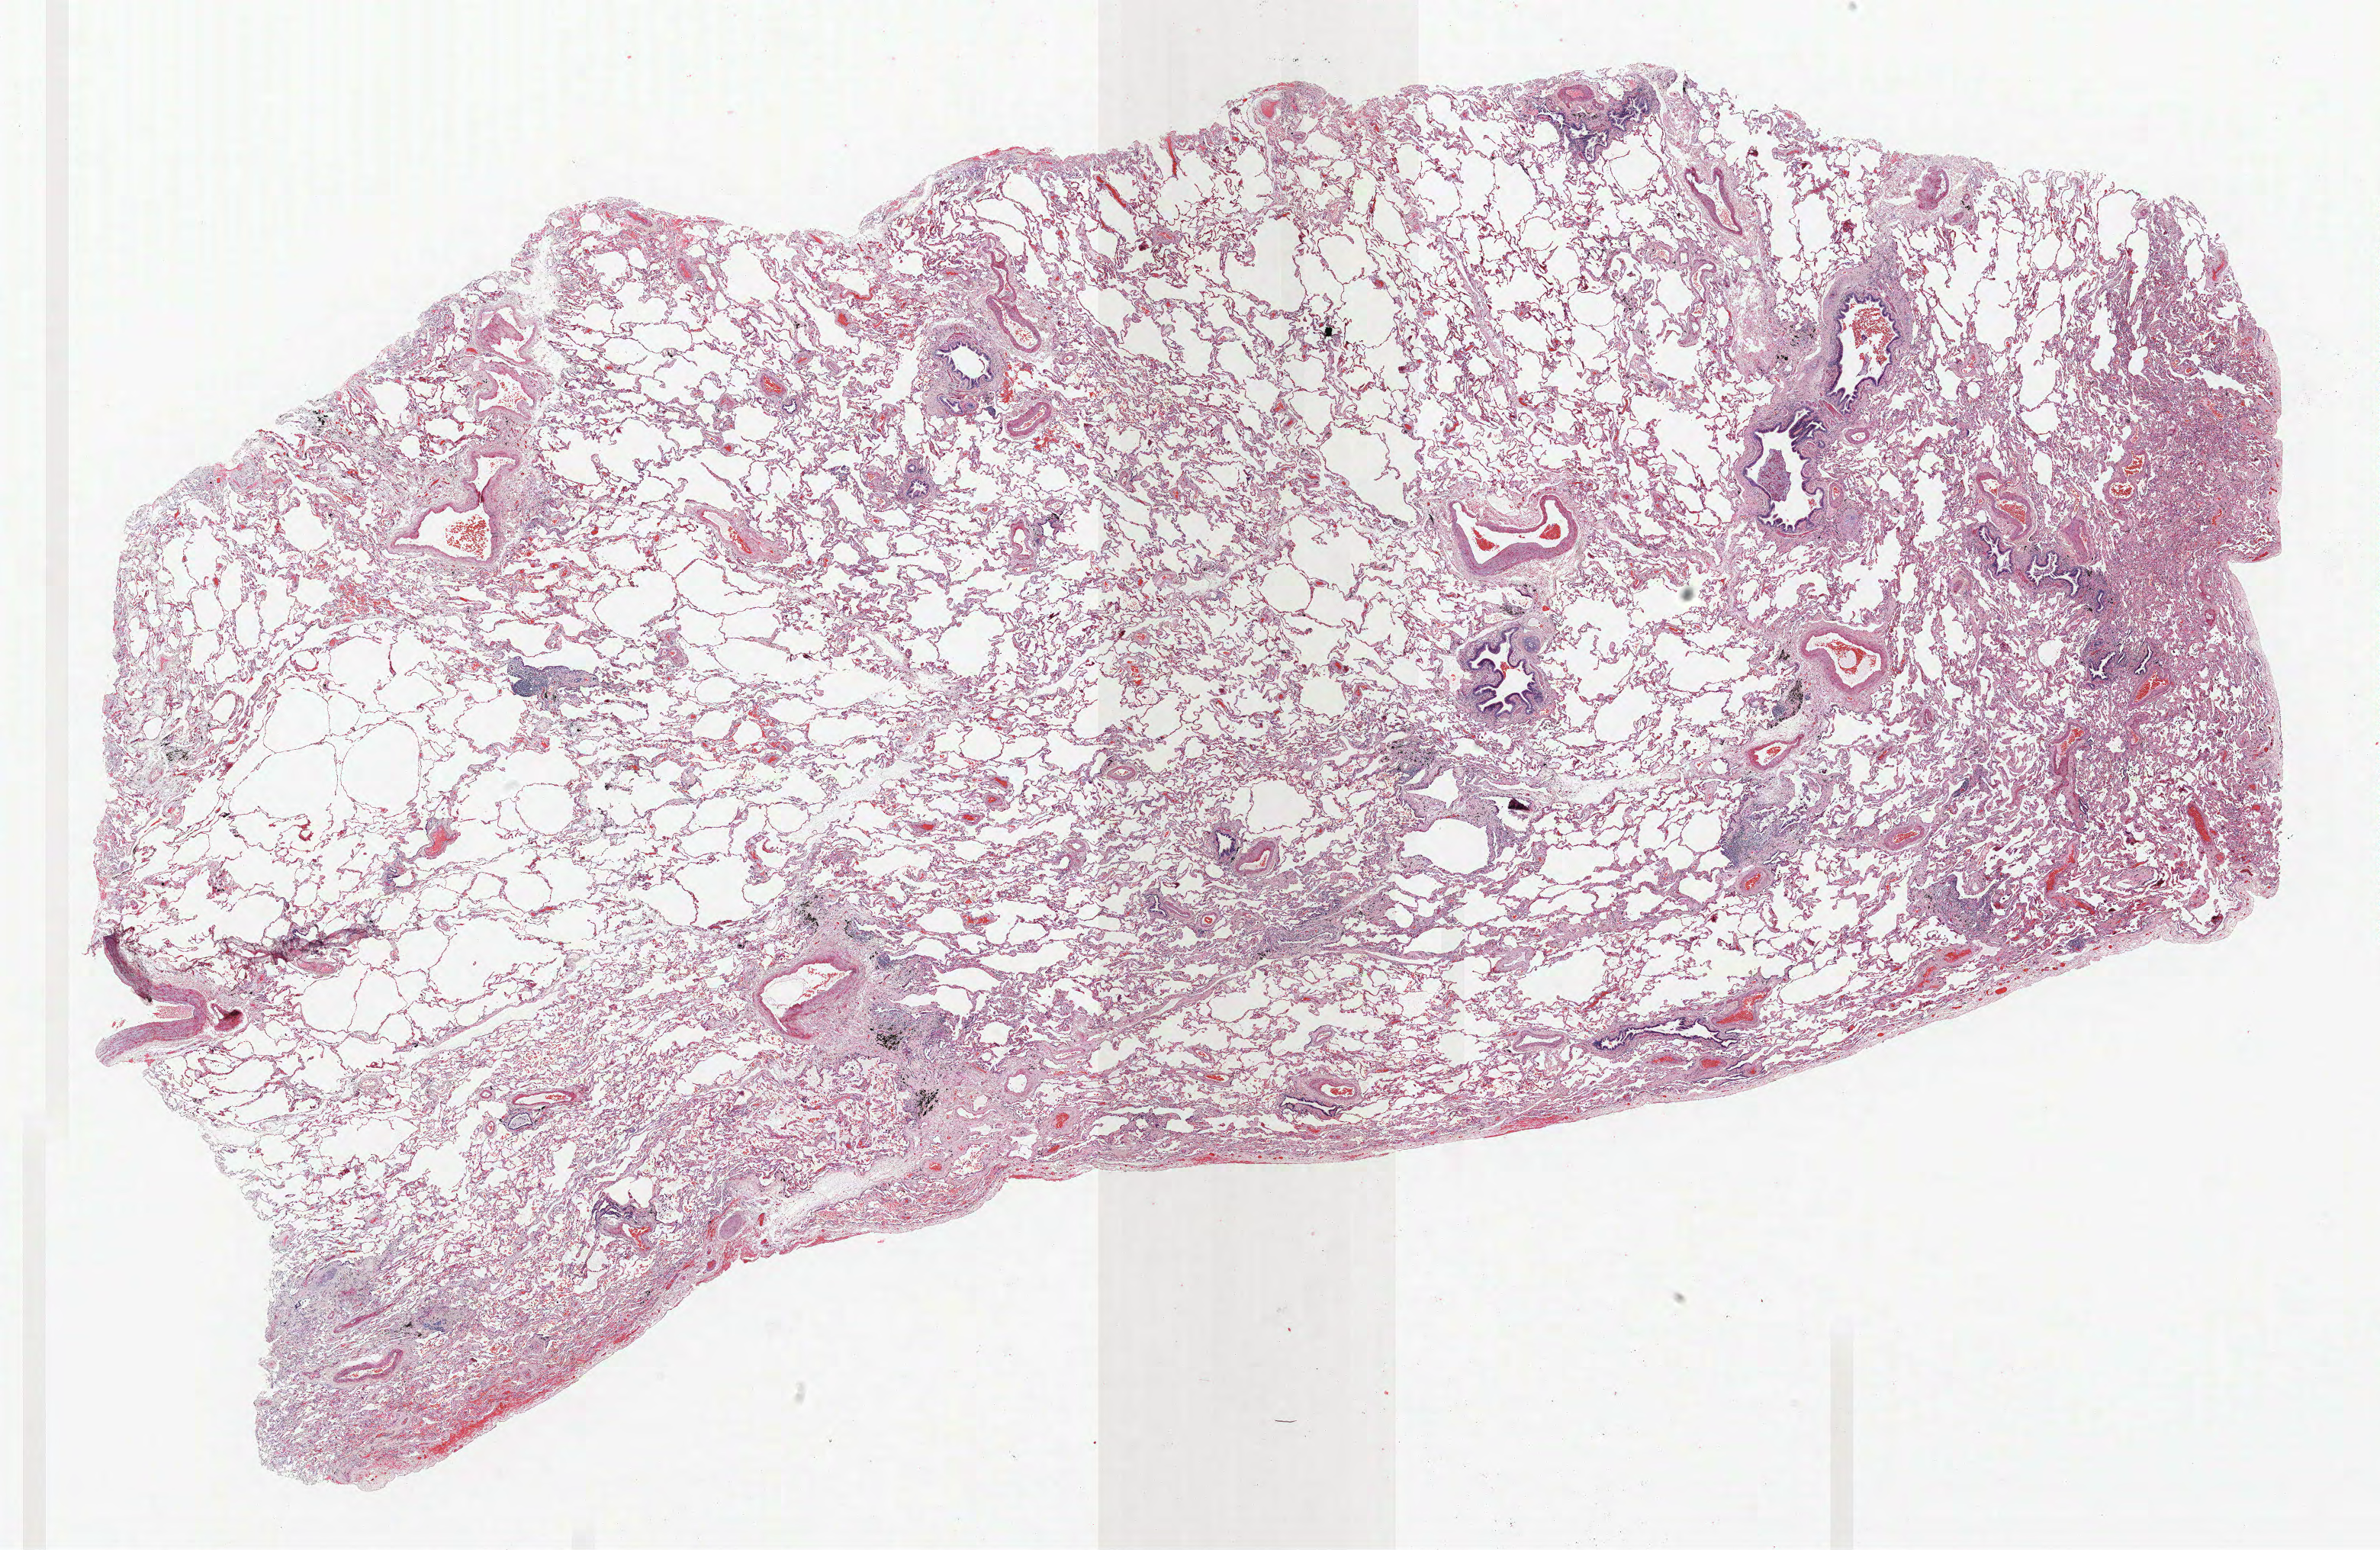
H&E whole-slide image, low-resolution overview of the scanned area, about 25.0 x 16.3 mm (acquisition: 40x scan), FFPE section, lung tissue. Female patient, aged 61 at enrolment. Former smoker at enrolment. Grade: poorly differentiated (G3).
Tumour size (pathology): 22 mm. Participant's lung-cancer diagnosis: Adenocarcinoma, NOS. Primary tumour location (clinical record): right upper lobe. Stage (AJCC 6th edition): IIIA.